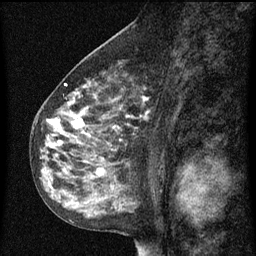
Breast MRI (dynamic contrast-enhanced), one sagittal slice. Slice 40 of 60 in the series (ordered by position). Dynamic contrast-enhanced series, image 2 of 3 at this slice position (ordered by acquisition). 1.5 T. TE 4.2 ms, TR 8 ms. 2 mm slice thickness. 256 × 256 image matrix, field of view 180 × 180 mm. Patient: female, 55 years.
Annotated regions visible in this slice (semi-automatically segmented with operator editing):
- analysis volume of interest (the breast-tissue region the enhancement analysis was run in; not a lesion): bounding box <34,68,151,151> (left, top, right, bottom; pixels)
- tumour enhancement mask (voxels above the 70 % enhancement threshold inside the analysis volume of interest): <48,84,149,149>